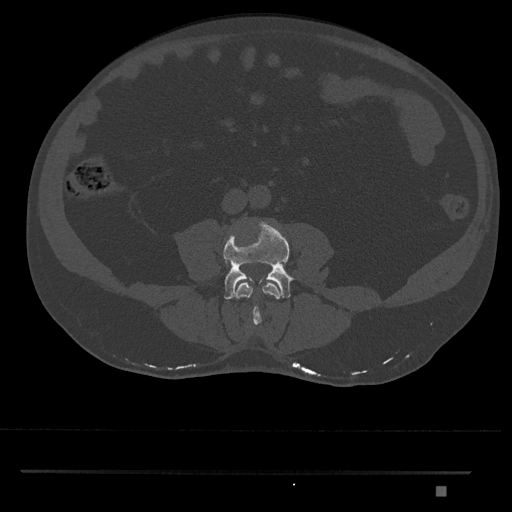
CT including the spine, one axial slice; slice 640 of 1134 in the series (ordered by position); reconstruction kernel Br40s/3; 120 kVp; bone window (W 1800 / L 400 HU); 0.5 mm slice thickness; 512 × 512 image matrix. Male patient, age 65 years. From the clinical record (not read from this slice): primary cancer: prostate.
Structures marked on this image (semi-automatically segmented with operator editing):
- L3 vertebra: bounding box (x1, y1, x2, y2) in pixels: (236, 282, 280, 325)
- L4 vertebra: (223, 221, 294, 299)